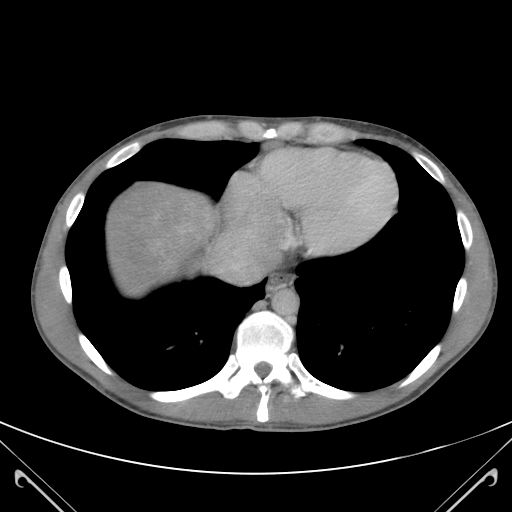
Contrast-enhanced abdominal CT (liver protocol), one axial slice; slice 108 of 118 in the series (ordered by position); 120 kVp; soft-tissue window (W 400 / L 40 HU); 3 mm slice thickness; 512 × 512 image matrix, field of view 380 × 380 mm. Case-level facts recorded for this patient, not image findings: diagnosis: hepatocellular carcinoma (patient treated with transarterial chemoembolisation; whether this scan precedes or follows treatment is not stated here); TNM stage (as recorded): Stage-IIIB; Child-Pugh class: A.
Outlined on this slice (semi-automatic segmentation, software-assisted and operator-edited):
- abdominal aorta: bounding box [x1, y1, x2, y2] px = [274, 292, 298, 314]
- liver parenchyma outside the tumour (the mass and vessels are separate outlines, so this box may not span the whole liver): [105, 183, 221, 287]